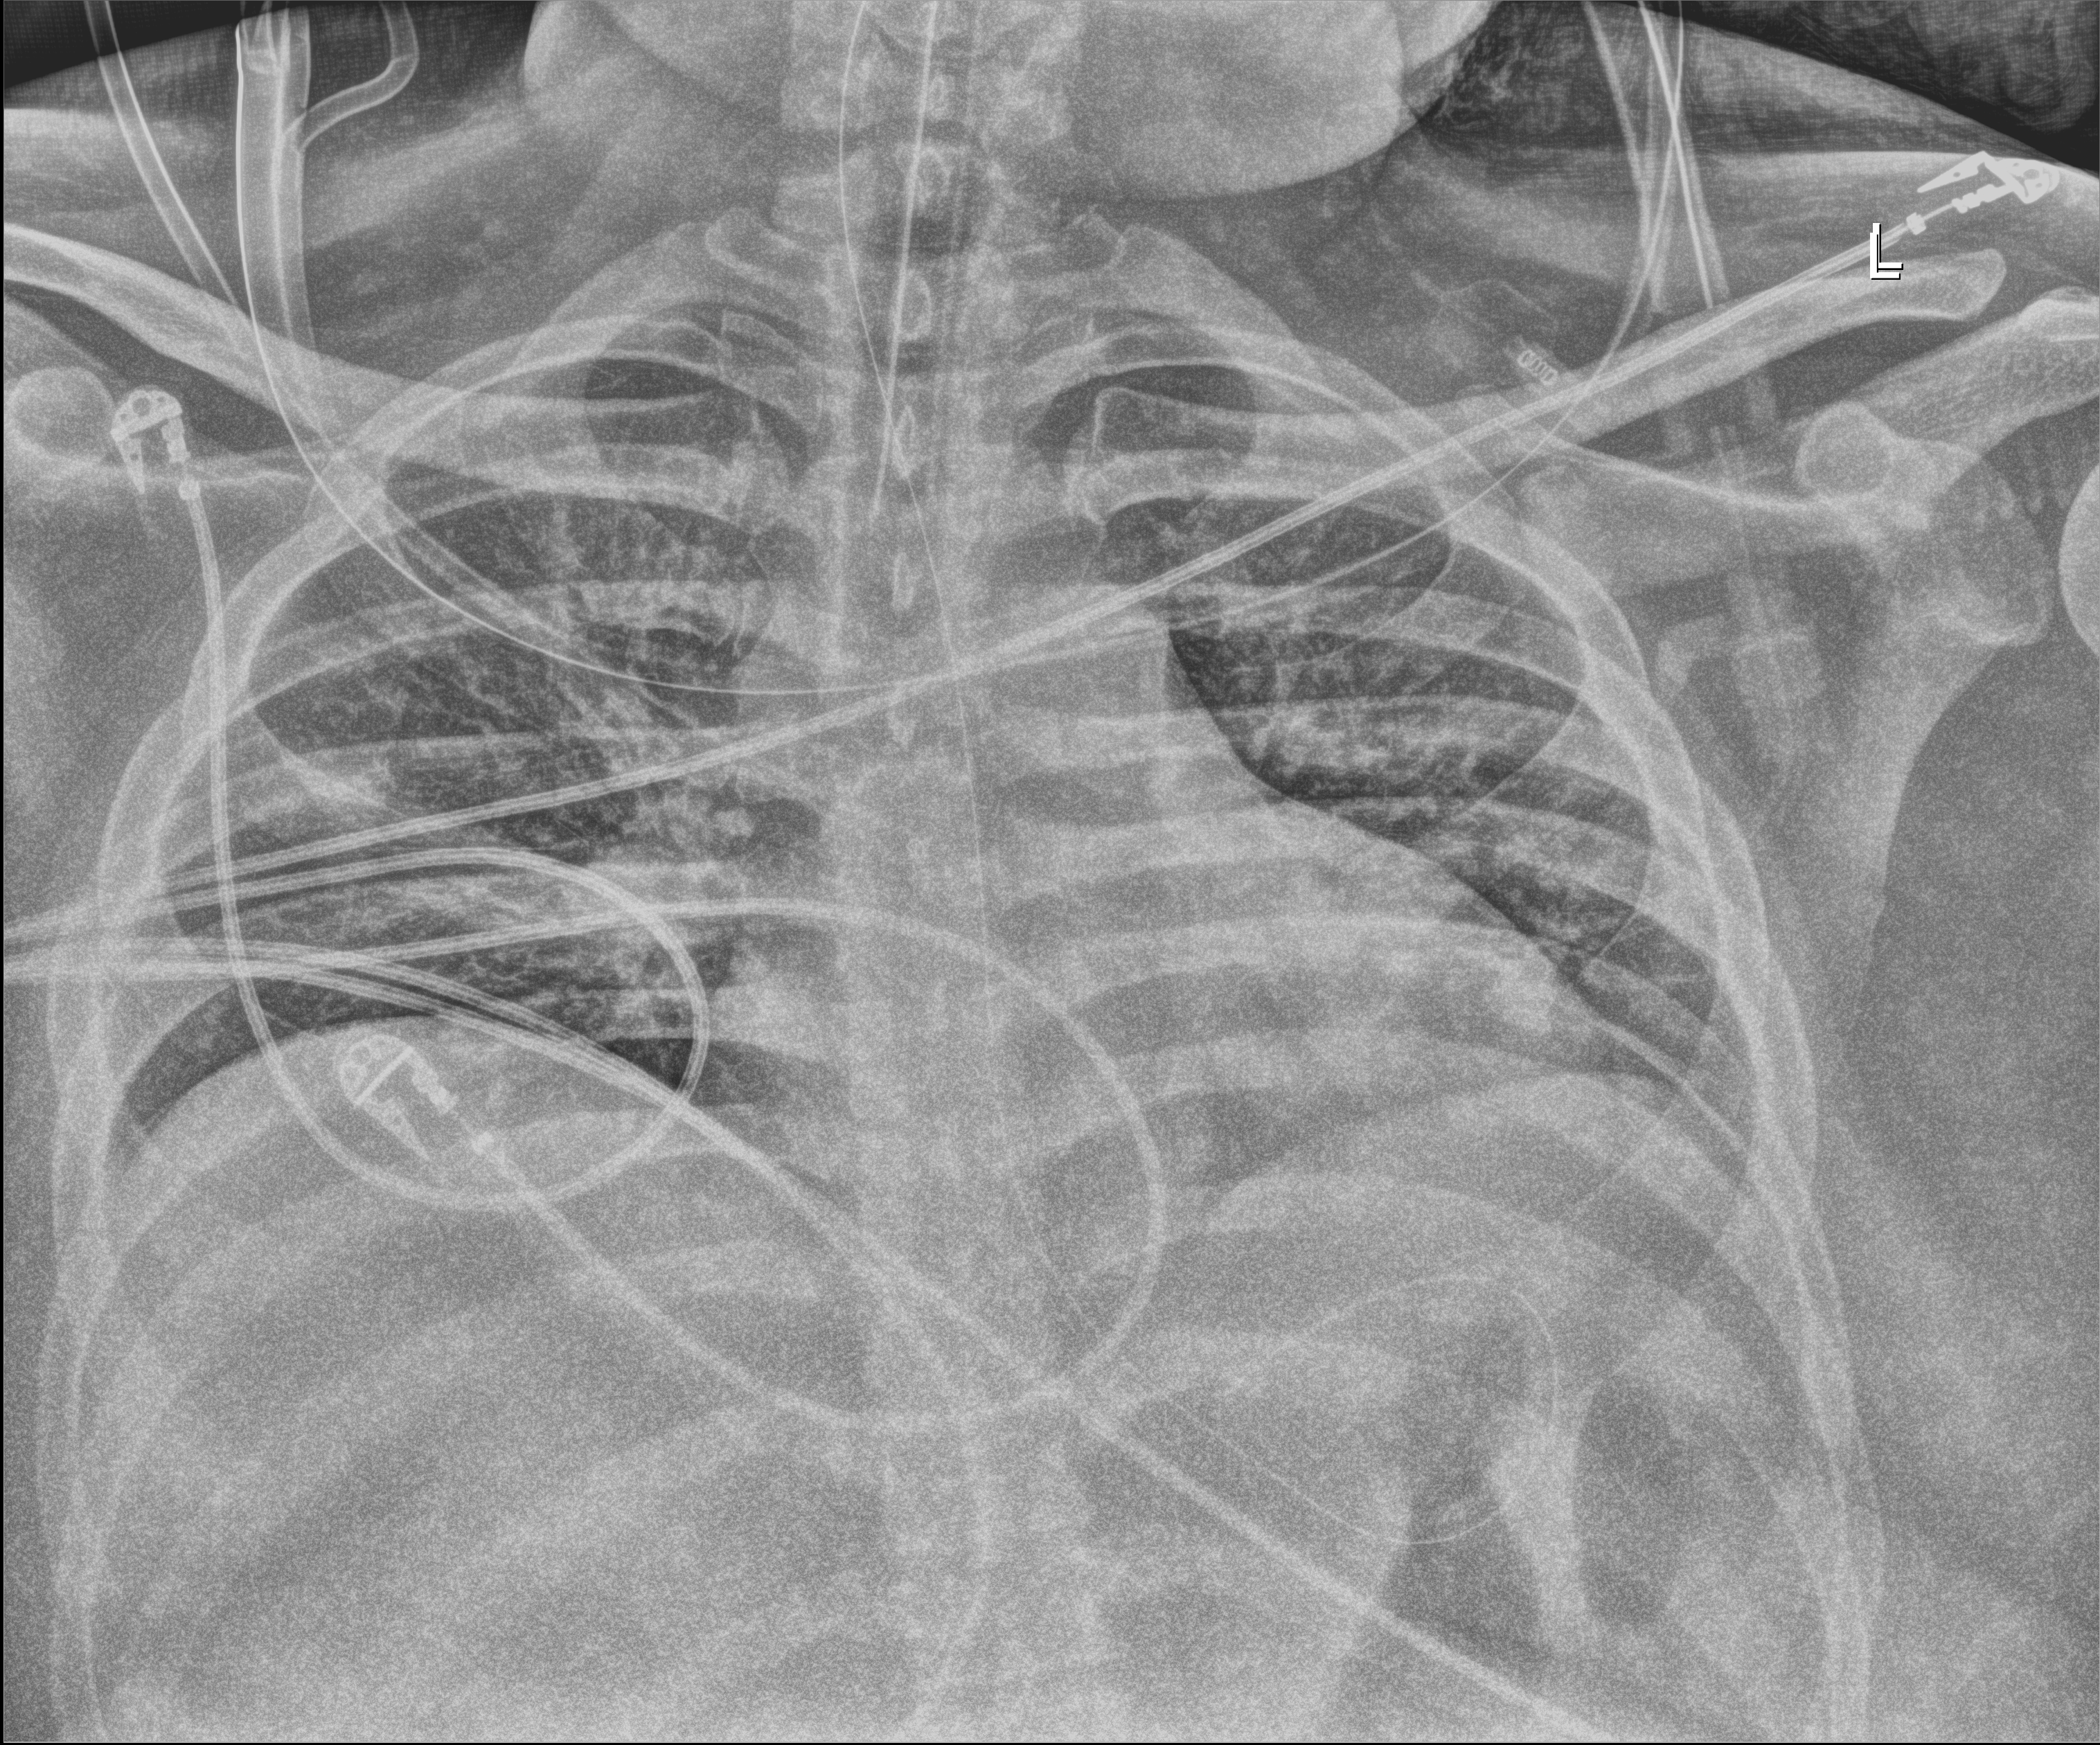
Chest X-ray (portable), anteroposterior (AP) projection. Patient hospitalised with COVID-19; male, aged 18–59 years.
Hospital-stay facts (about this admission, not read from this image; timing relative to this image not recorded): admitted to intensive care during this hospital stay: yes; mechanically ventilated during this hospital stay: yes.